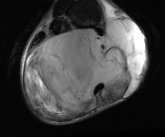
MRI of an extremity soft-tissue mass, one axial slice; position 25 of 81 along the scan axis; T2-weighted fat-saturated; MR volume resampled by the dataset authors to the PET/CT grid (not the native acquisition matrix); 3.27 mm slice thickness; 165 × 137 image matrix, field of view 161 × 134 mm. Male patient. Case-level facts recorded for this patient, not image findings: histological type: liposarcoma - round cell; grade: high; site of the primary tumour: right calf.
Outlined on this slice (expert contour drawn on MRI and transferred to this co-registered scan by the dataset authors):
- gross tumour volume (mass): bounding box [x1, y1, x2, y2] px = [23, 18, 147, 117]